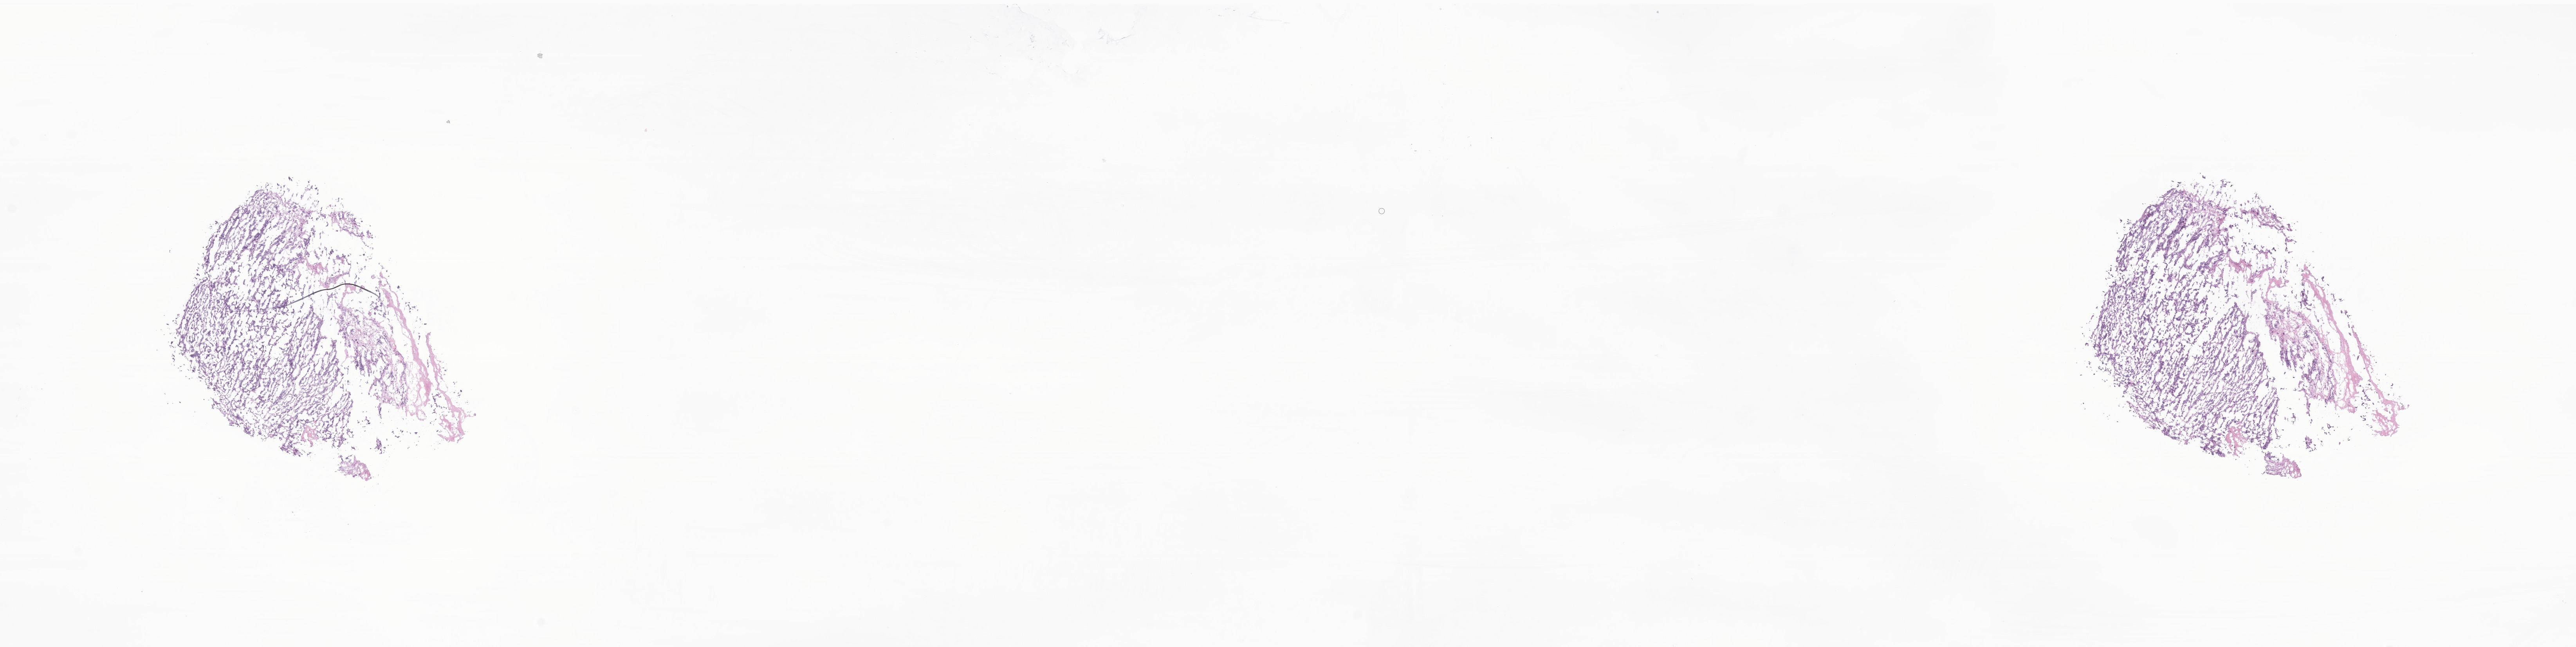
Digitized hematoxylin and eosin (H&E)-stained section of tumor tissue from the thyroid, low-resolution overview of the scanned area, about 27.7 x 7.0 mm; cryosection (OCT / tissue freezing medium). Patient female; age 185 months (15 years 5 months).
Diagnosis: Papillary carcinoma, NOS.